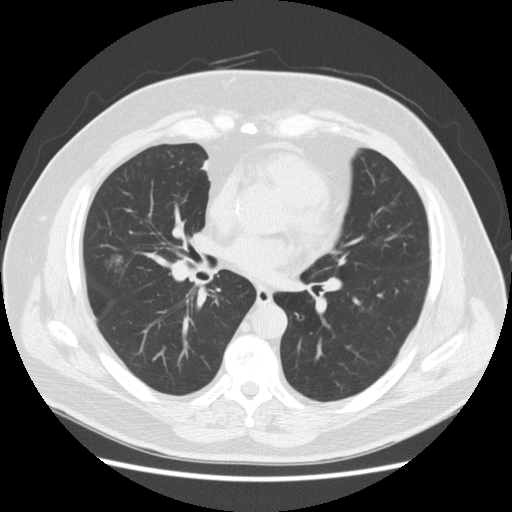
Low-dose screening chest CT, axial slice; baseline screening round; lung window (W 1500 / L -600 HU); 2.5 mm slice thickness; 120 kVp; slice 113 of 213 in the series; 512 × 512 image matrix. Male participant, aged 67 years at enrolment.
• Expert reader's lesion annotation, bounding box [x1, y1, x2, y2] px = [88, 248, 134, 295].
• Screening reader's record for this exam (one nodule recorded; not confirmed to be the boxed lesion): non-calcified nodule or mass ≥4 mm, right middle lobe, 15 × 11 mm, smooth margins, soft tissue attenuation.
• Participant outcome: lung cancer diagnosed 409 days after this screen (after the second annual screen) — adenocarcinoma, NOS, right middle lobe, moderately differentiated (G2), stage IA (AJCC 6th edition), 14 mm at pathology.